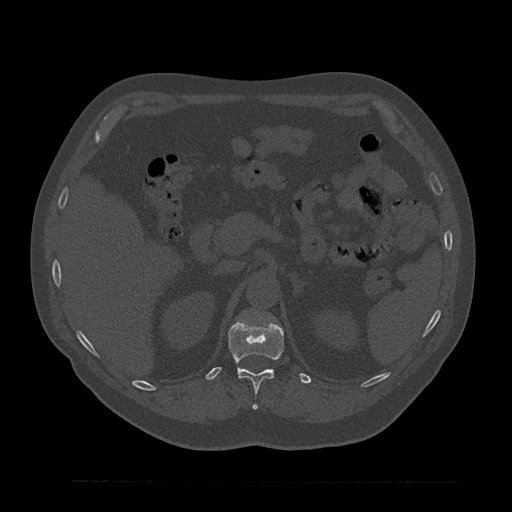
CT including the spine, one axial slice. Position 221 of 797 along the scan axis. Reconstruction kernel Br40s/3. Bone window (W 1800 / L 400 HU). 0.5 mm slice thickness. 512 × 512 image matrix, field of view 430 × 430 mm. Male patient, age 61 years. Case-level facts recorded for this patient, not image findings: primary cancer: prostate.
Structures marked on this image (semi-automatically segmented with operator editing):
- T12 vertebra: bounding box [x1, y1, x2, y2] px = [228, 319, 284, 409]